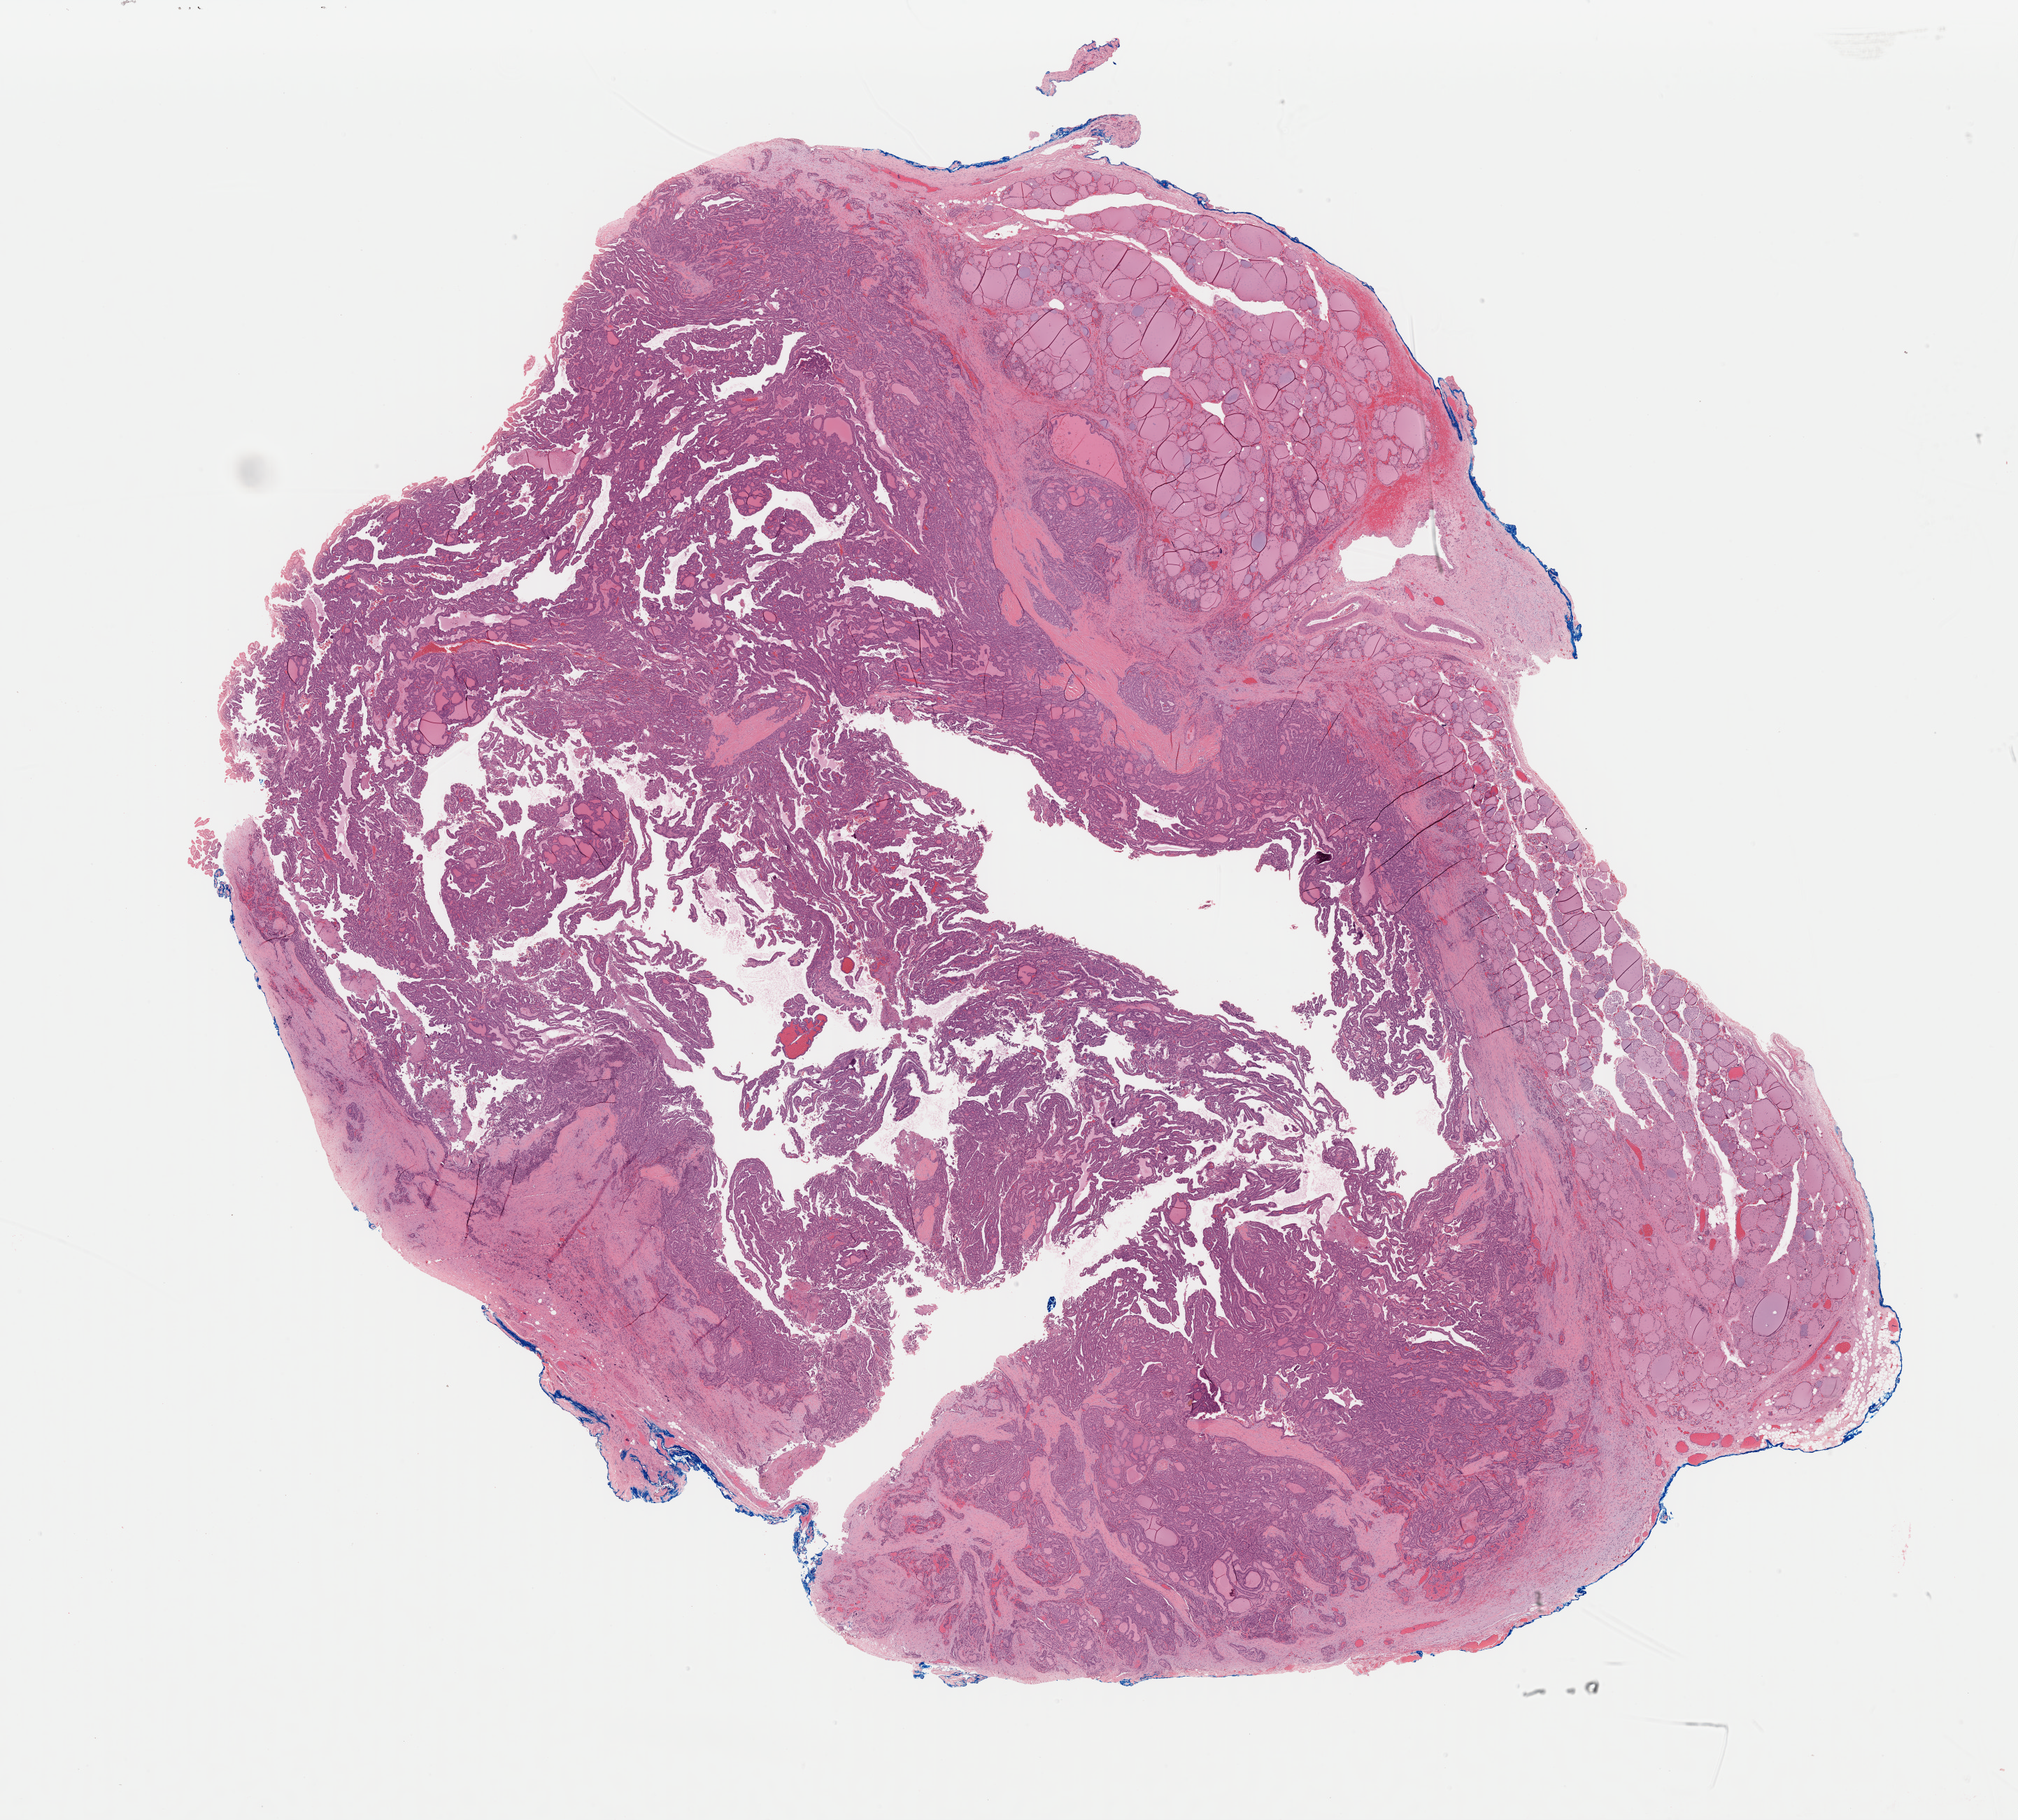
Whole-slide histology image, Hematoxylin and eosin (H&E) stained, whole scanned area (about 22.8 x 20.6 mm, from a 40x scan) shown as a low-resolution overview, formalin-fixed paraffin-embedded (FFPE) diagnostic section, thyroid, primary tumour sample. Patient: female, age at initial diagnosis 37 years.
* AJCC pathologic stage: I (5th edition)
* pathologic diagnosis: Papillary adenocarcinoma, NOS (thyroid gland)